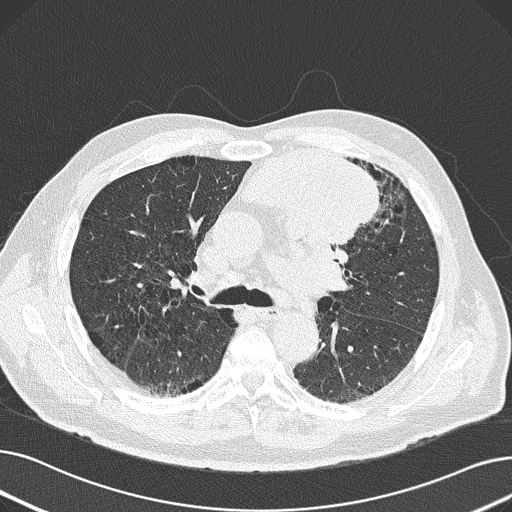
Axial slice from a low-dose chest CT screening exam; baseline screening round; lung window (W 1500 / L -600 HU); slice 68 of 165 in the series. Male, age 69 years at enrolment.
Expert-annotated lung lesion, bounding box <232,138,382,251> (left, top, right, bottom; pixels). Screening reader's record for this exam (one nodule recorded; not confirmed to be the boxed lesion): non-calcified nodule or mass ≥4 mm, left upper lobe, 6 × 10 mm, spiculated (stellate) margins, soft tissue attenuation. Lung cancer was diagnosed 20 days after this screen: non-small cell carcinoma, left upper lobe, poorly differentiated (G3), stage IB (AJCC 6th edition), 100 mm at pathology.